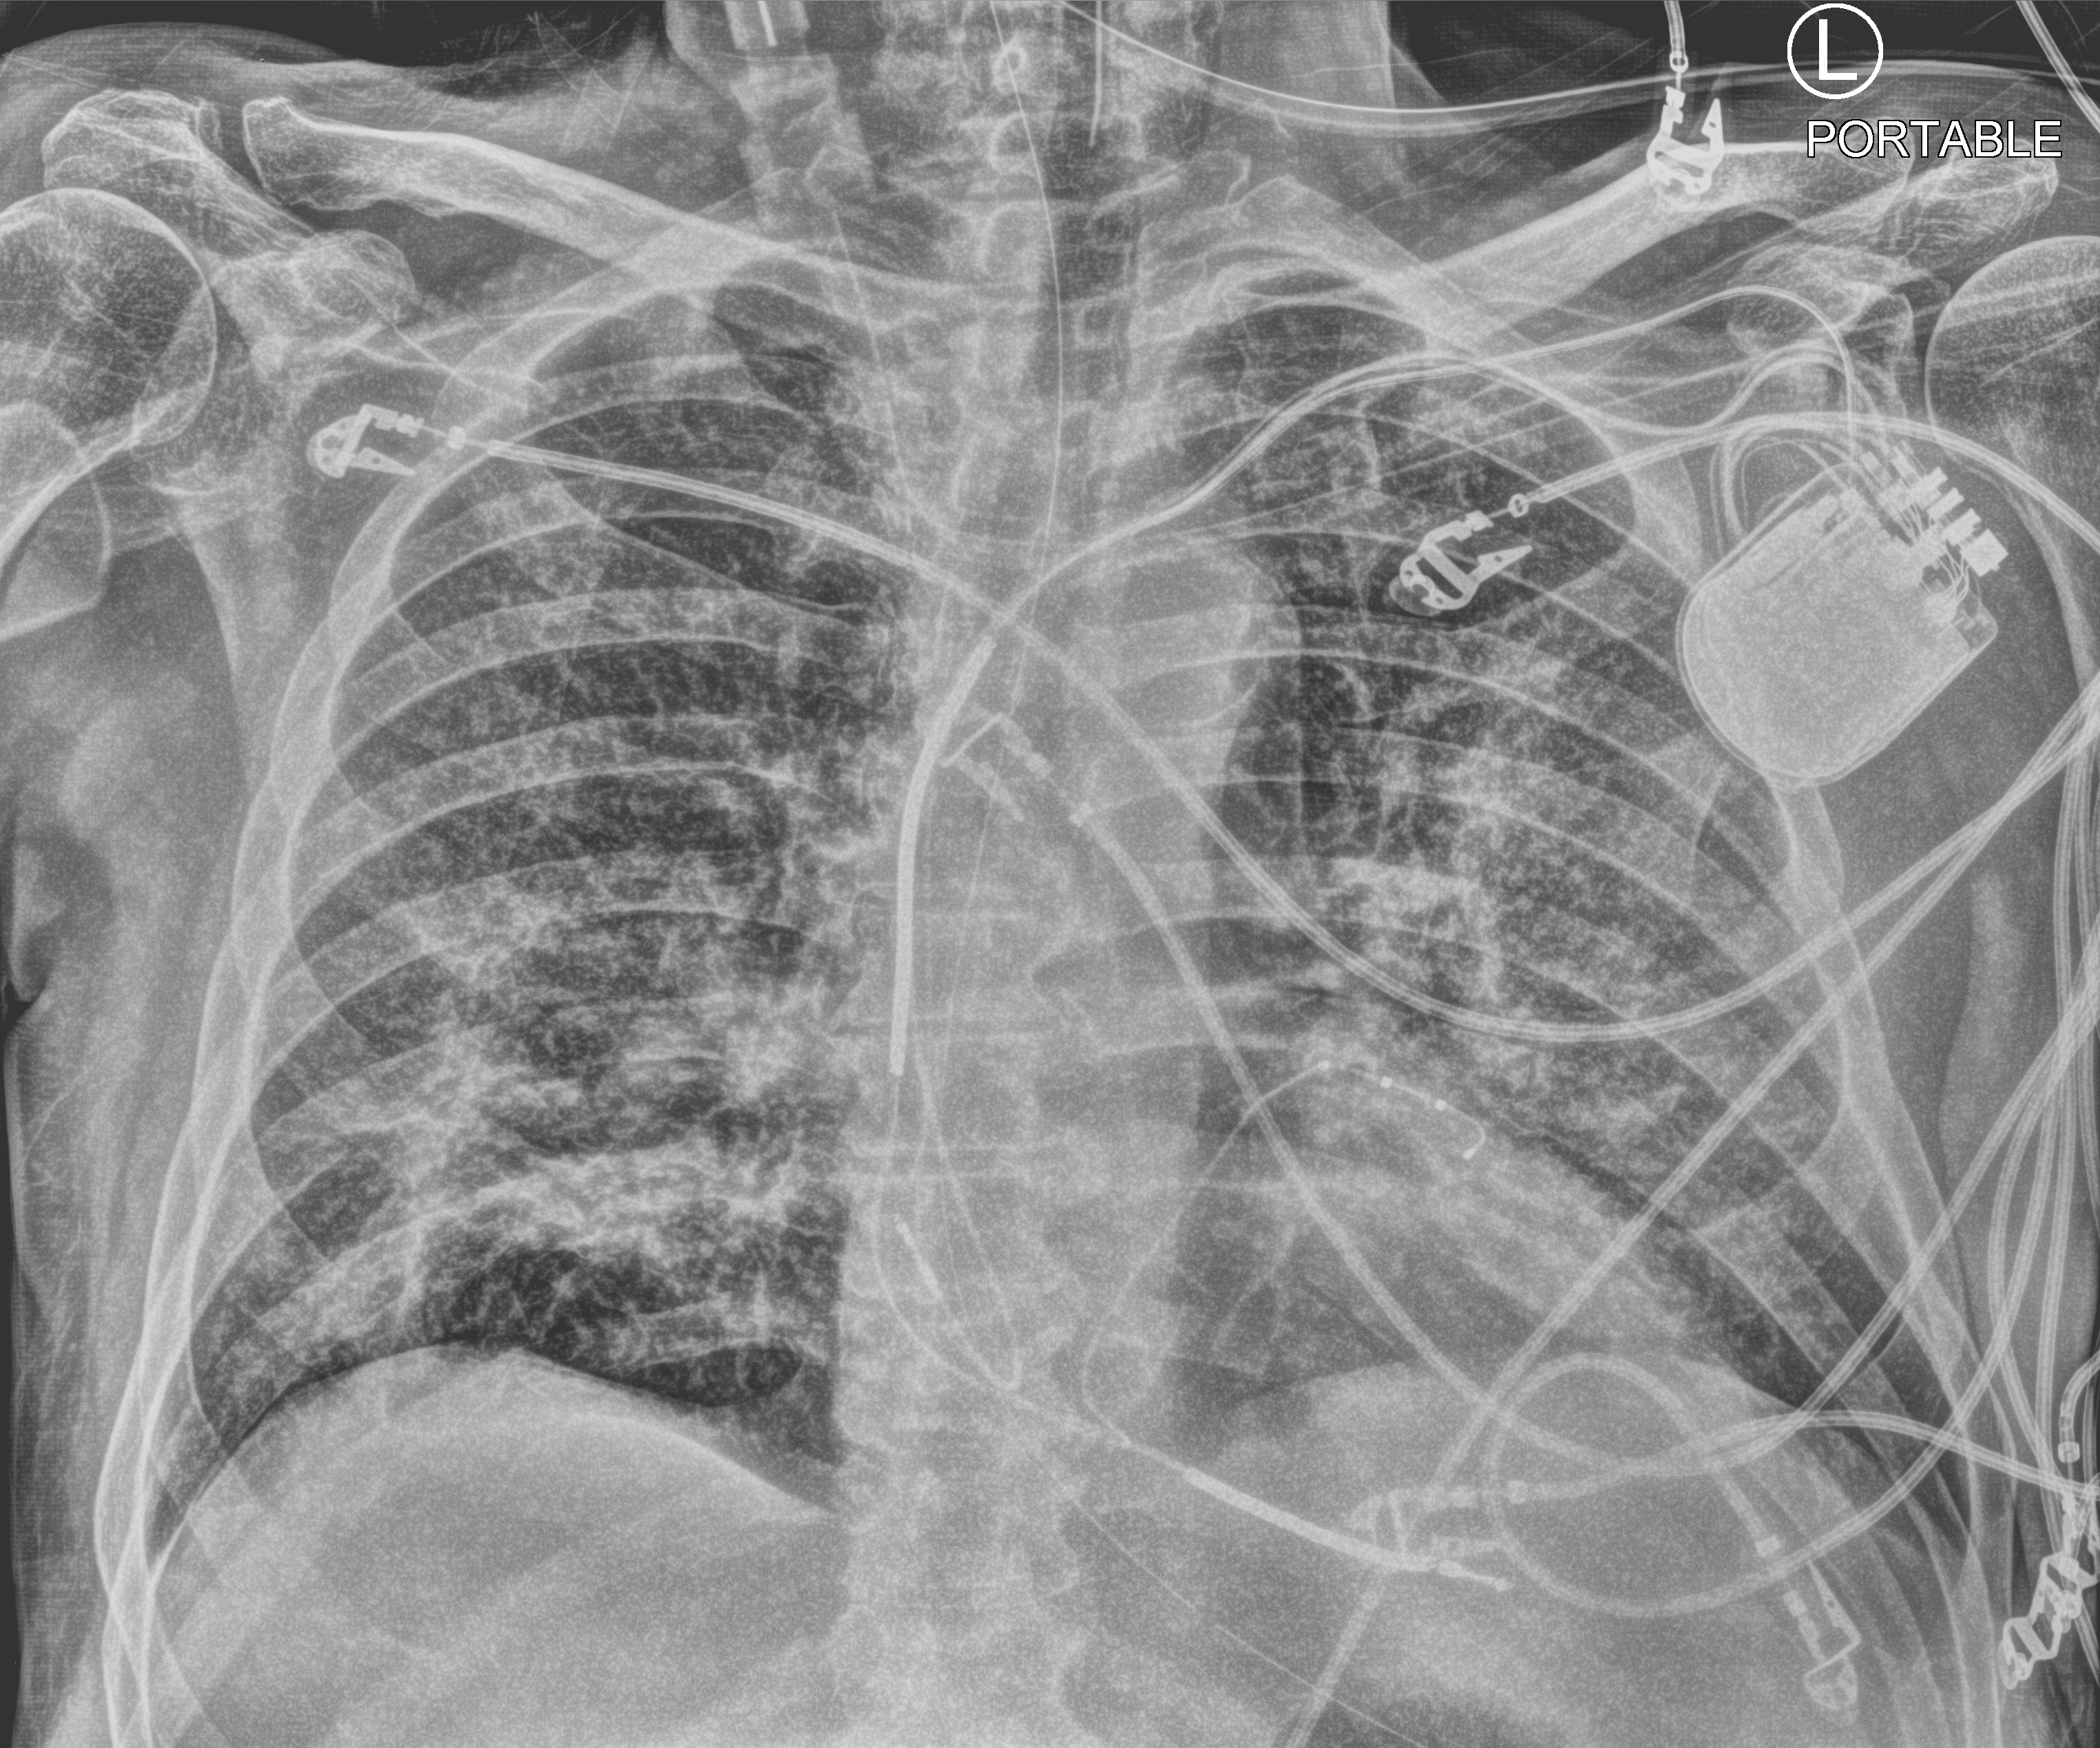
Portable chest radiograph. Male patient hospitalised with COVID-19, age 60–74 years.
Admission-level facts for this patient (not findings on this image; timing relative to this image not recorded):
- admitted to intensive care during this hospital stay: yes
- mechanically ventilated during this hospital stay: yes